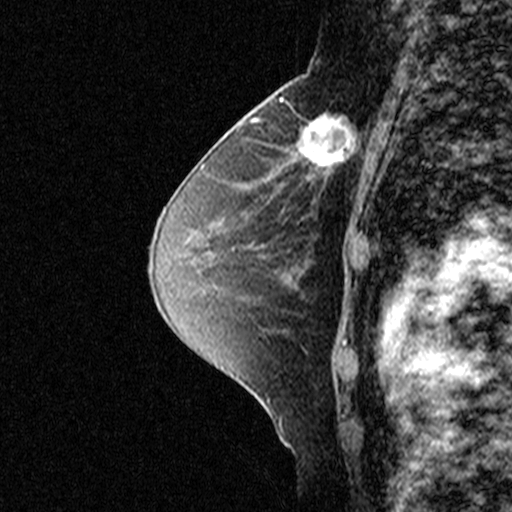
Breast MRI (dynamic contrast-enhanced), one sagittal slice. Position 25 of 44 along the scan axis. Dynamic contrast-enhanced study with each time point stored as its own series, time point 2 of 3 at this slice position (early post-contrast, ordered by acquisition time). 1.5 T. TE 4.5 ms, TR 11 ms. 512 × 512 image matrix. Patient: female, 49 years. Case-level facts recorded for this patient, not image findings: setting: breast cancer imaged before/during neoadjuvant chemotherapy; receptor status: triple-negative.
Annotated regions visible in this slice (semi-automatically segmented with operator editing):
- analysis volume of interest (the breast-tissue region the enhancement analysis was run in; not a lesion): bounding box (x1, y1, x2, y2) in pixels: (276, 94, 369, 181)
- tumour enhancement mask (voxels above the 90 % enhancement threshold inside the analysis volume of interest): (307, 114, 348, 164)